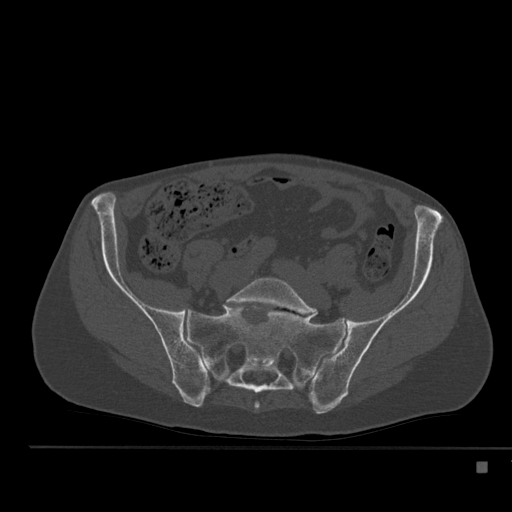
CT including the spine, one axial slice. Position 106 of 517 along the scan axis. Reconstruction kernel Br40s. 120 kVp. Bone window (W 1800 / L 400 HU). 512 × 512 image matrix, field of view 408 × 408 mm. Patient: male, 70 years. From the clinical record (not read from this slice): primary cancer: renal.
Structures marked on this image (semi-automatic segmentation, software-assisted and operator-edited):
- L5 vertebra: box from (x=226, y=277) to (x=317, y=316) px